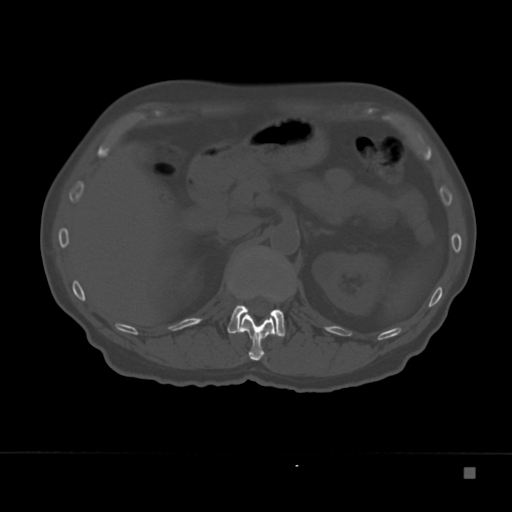
CT including the spine, one axial slice; position 121 of 332 along the scan axis; reconstruction kernel Br40s; 120 kVp; bone window (W 1800 / L 400 HU); 1.5 mm slice thickness; 512 × 512 image matrix. Patient: male, 72 years. Case-level facts recorded for this patient, not image findings: primary cancer: skeletal.
Structures marked on this image (semi-automatically segmented with operator editing):
- L1 vertebra: box from (x=227, y=295) to (x=285, y=337) px
- T12 vertebra: (x=240, y=290)–(x=276, y=361)